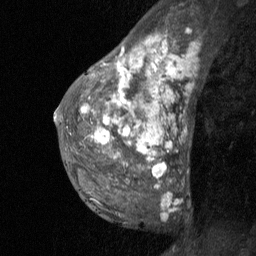
Breast MRI (dynamic contrast-enhanced), one sagittal slice; position 39 of 64 along the scan axis; dynamic contrast-enhanced study with each time point stored as its own series, time point 2 of 3 at this slice position (early post-contrast, ordered by acquisition time); 1.5 T; TE 4.8 ms, TR 27 ms; 2 mm slice thickness; 256 × 256 image matrix, field of view 180 × 180 mm. Female patient, age 36 years. From the clinical record (not read from this slice): setting: breast cancer imaged before/during neoadjuvant chemotherapy; receptor status: HR-positive, HER2-negative.
Outlined on this slice (semi-automatically segmented with operator editing):
- analysis volume of interest (the breast-tissue region the enhancement analysis was run in; not a lesion): bounding box [x1, y1, x2, y2] px = [67, 12, 196, 221]
- tumour enhancement mask (voxels above the 90 % enhancement threshold inside the analysis volume of interest): [83, 38, 159, 171]